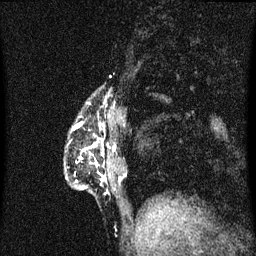
Breast MRI (dynamic contrast-enhanced), one sagittal slice. Slice 13 of 60 in the series (ordered by position). Dynamic contrast-enhanced series, image 2 of 3 at this slice position (ordered by acquisition). 1.5 T. TE 4.2 ms, TR 8.4 ms. 2 mm slice thickness. 256 × 256 image matrix, field of view 200 × 200 mm. Female patient, age 40 years.
Outlined on this slice (semi-automatically segmented with operator editing):
- analysis volume of interest (the breast-tissue region the enhancement analysis was run in; not a lesion): bounding box <65,102,108,195> (left, top, right, bottom; pixels)
- tumour enhancement mask (voxels above the 70 % enhancement threshold inside the analysis volume of interest): <73,124,107,181>